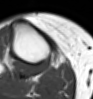
MRI of an extremity soft-tissue mass, one axial slice; MR volume resampled by the dataset authors to the PET/CT grid (not the native acquisition matrix); 3.27 mm slice thickness; 93 × 99 image matrix, field of view 91 × 97 mm. Female patient. From the clinical record (not read from this slice): histological type: undifferentiated – high grade; grade: high; site of the primary tumour: right thigh.
Structures marked on this image (expert contour drawn on MRI and transferred to this co-registered scan by the dataset authors):
- gross tumour volume (mass): box from (x=52, y=59) to (x=58, y=65) px